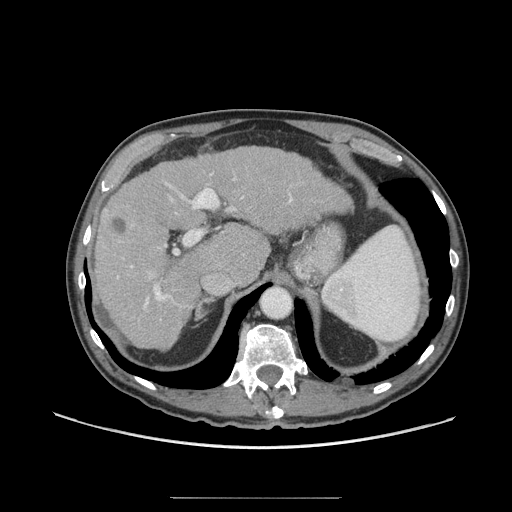
Contrast-enhanced abdominal CT (liver protocol), one axial slice; slice 47 of 71 in the series (ordered by position); reconstruction kernel STANDARD; 140 kVp; soft-tissue window (W 400 / L 40 HU); 512 × 512 image matrix, field of view 400 × 400 mm. From the clinical record (not read from this slice): diagnosis: hepatocellular carcinoma (patient treated with transarterial chemoembolisation; whether this scan precedes or follows treatment is not stated here); TNM stage (as recorded): Stage-I; Child-Pugh class: A; tumour nodularity: uninodular; tumour size: 3.5 cm.
Outlined on this slice (semi-automatic segmentation, software-assisted and operator-edited):
- liver parenchyma outside the tumour (the mass and vessels are separate outlines, so this box may not span the whole liver): bounding box (x1, y1, x2, y2) in pixels: (94, 146, 348, 348)
- mass: (98, 206, 135, 253)
- liver vessels: (117, 174, 293, 309)